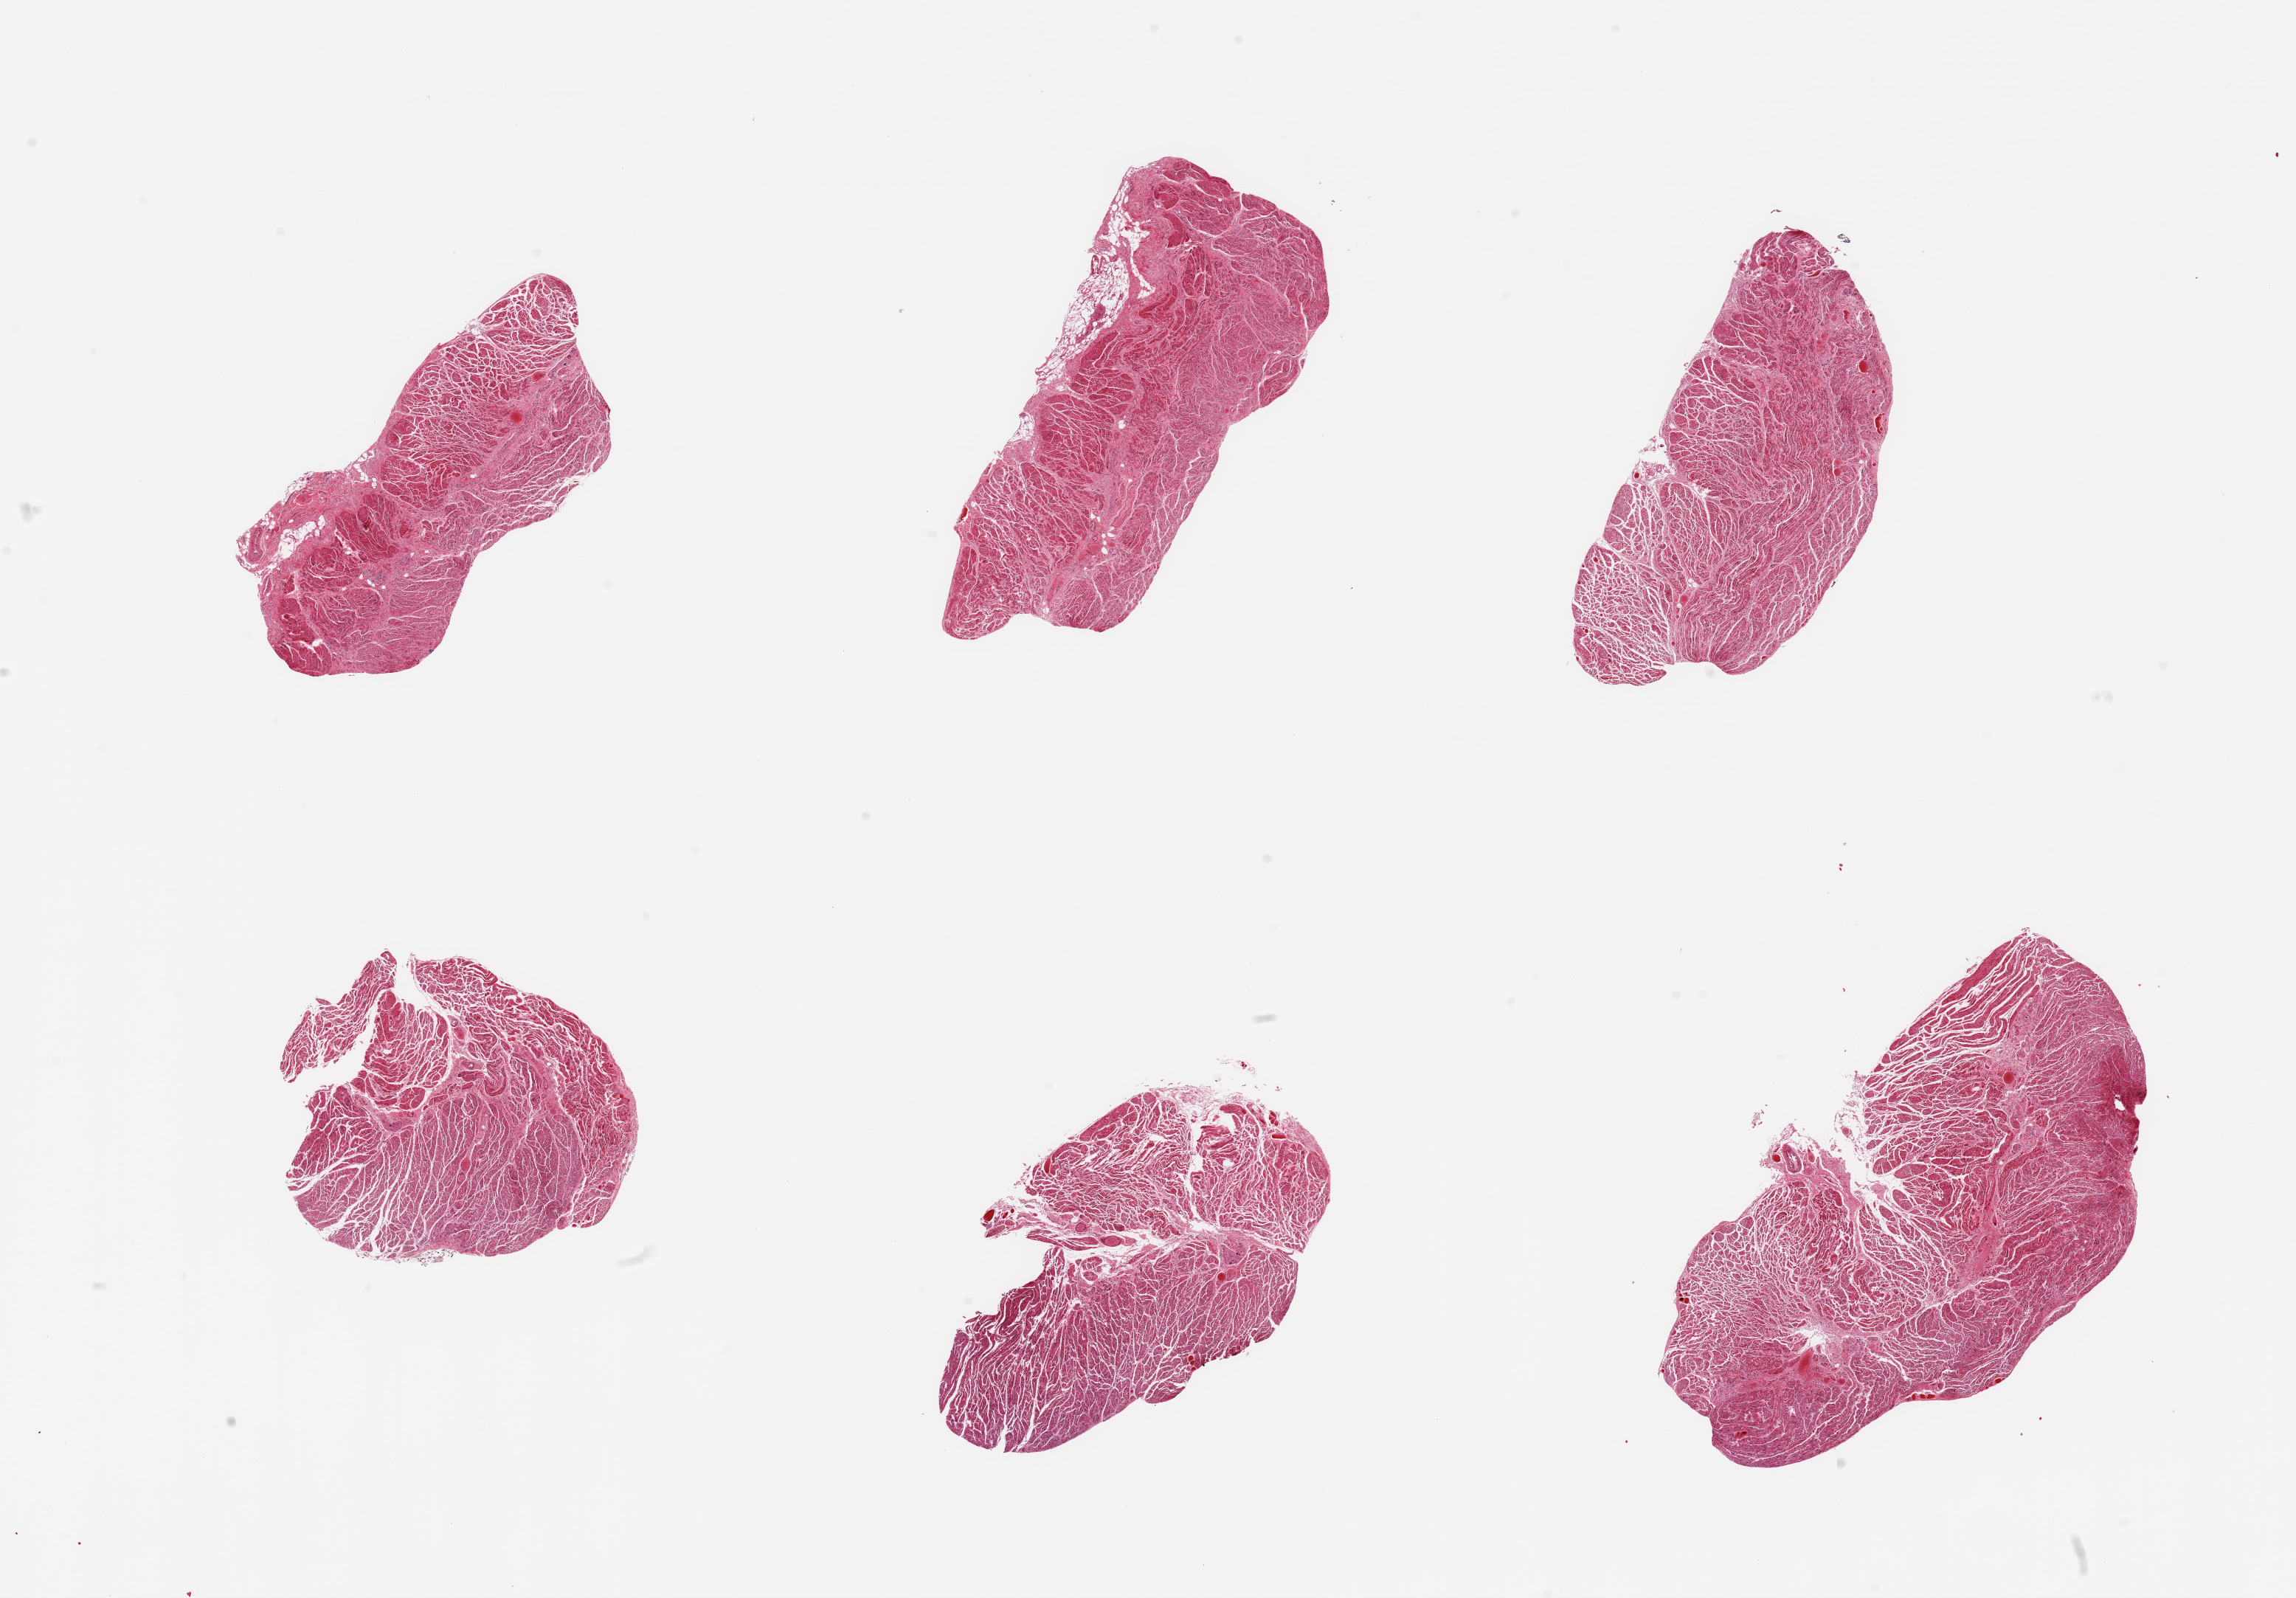
H&E whole-slide image, whole scanned area (about 24.6 x 17.1 mm) shown as a low-resolution overview; PAXgene-fixed paraffin-embedded (PFPE) section; section of gastroesophageal junction (target tissue); tissue donor sample. Donor: male.
Pathologist's review note for this sample: 6 pieces, donfirmed target muscularis.